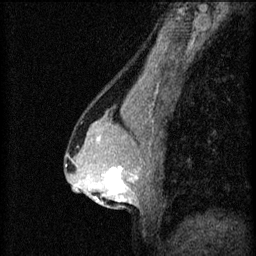
Breast MRI (dynamic contrast-enhanced), one sagittal slice; slice 36 of 60 in the series (ordered by position); 3 images stored at this slice position (order not interpretable as contrast timing); 1.5 T; TE 4.2 ms, TR 8.2 ms; 2 mm slice thickness; 256 × 256 image matrix, field of view 180 × 180 mm. Female patient, age 44 years.
Annotated regions visible in this slice (semi-automatic segmentation, software-assisted and operator-edited):
- analysis volume of interest (the breast-tissue region the enhancement analysis was run in; not a lesion): box from (x=94, y=162) to (x=143, y=205) px
- tumour enhancement mask (voxels above the 70 % enhancement threshold inside the analysis volume of interest): (x=94, y=166)–(x=139, y=203)